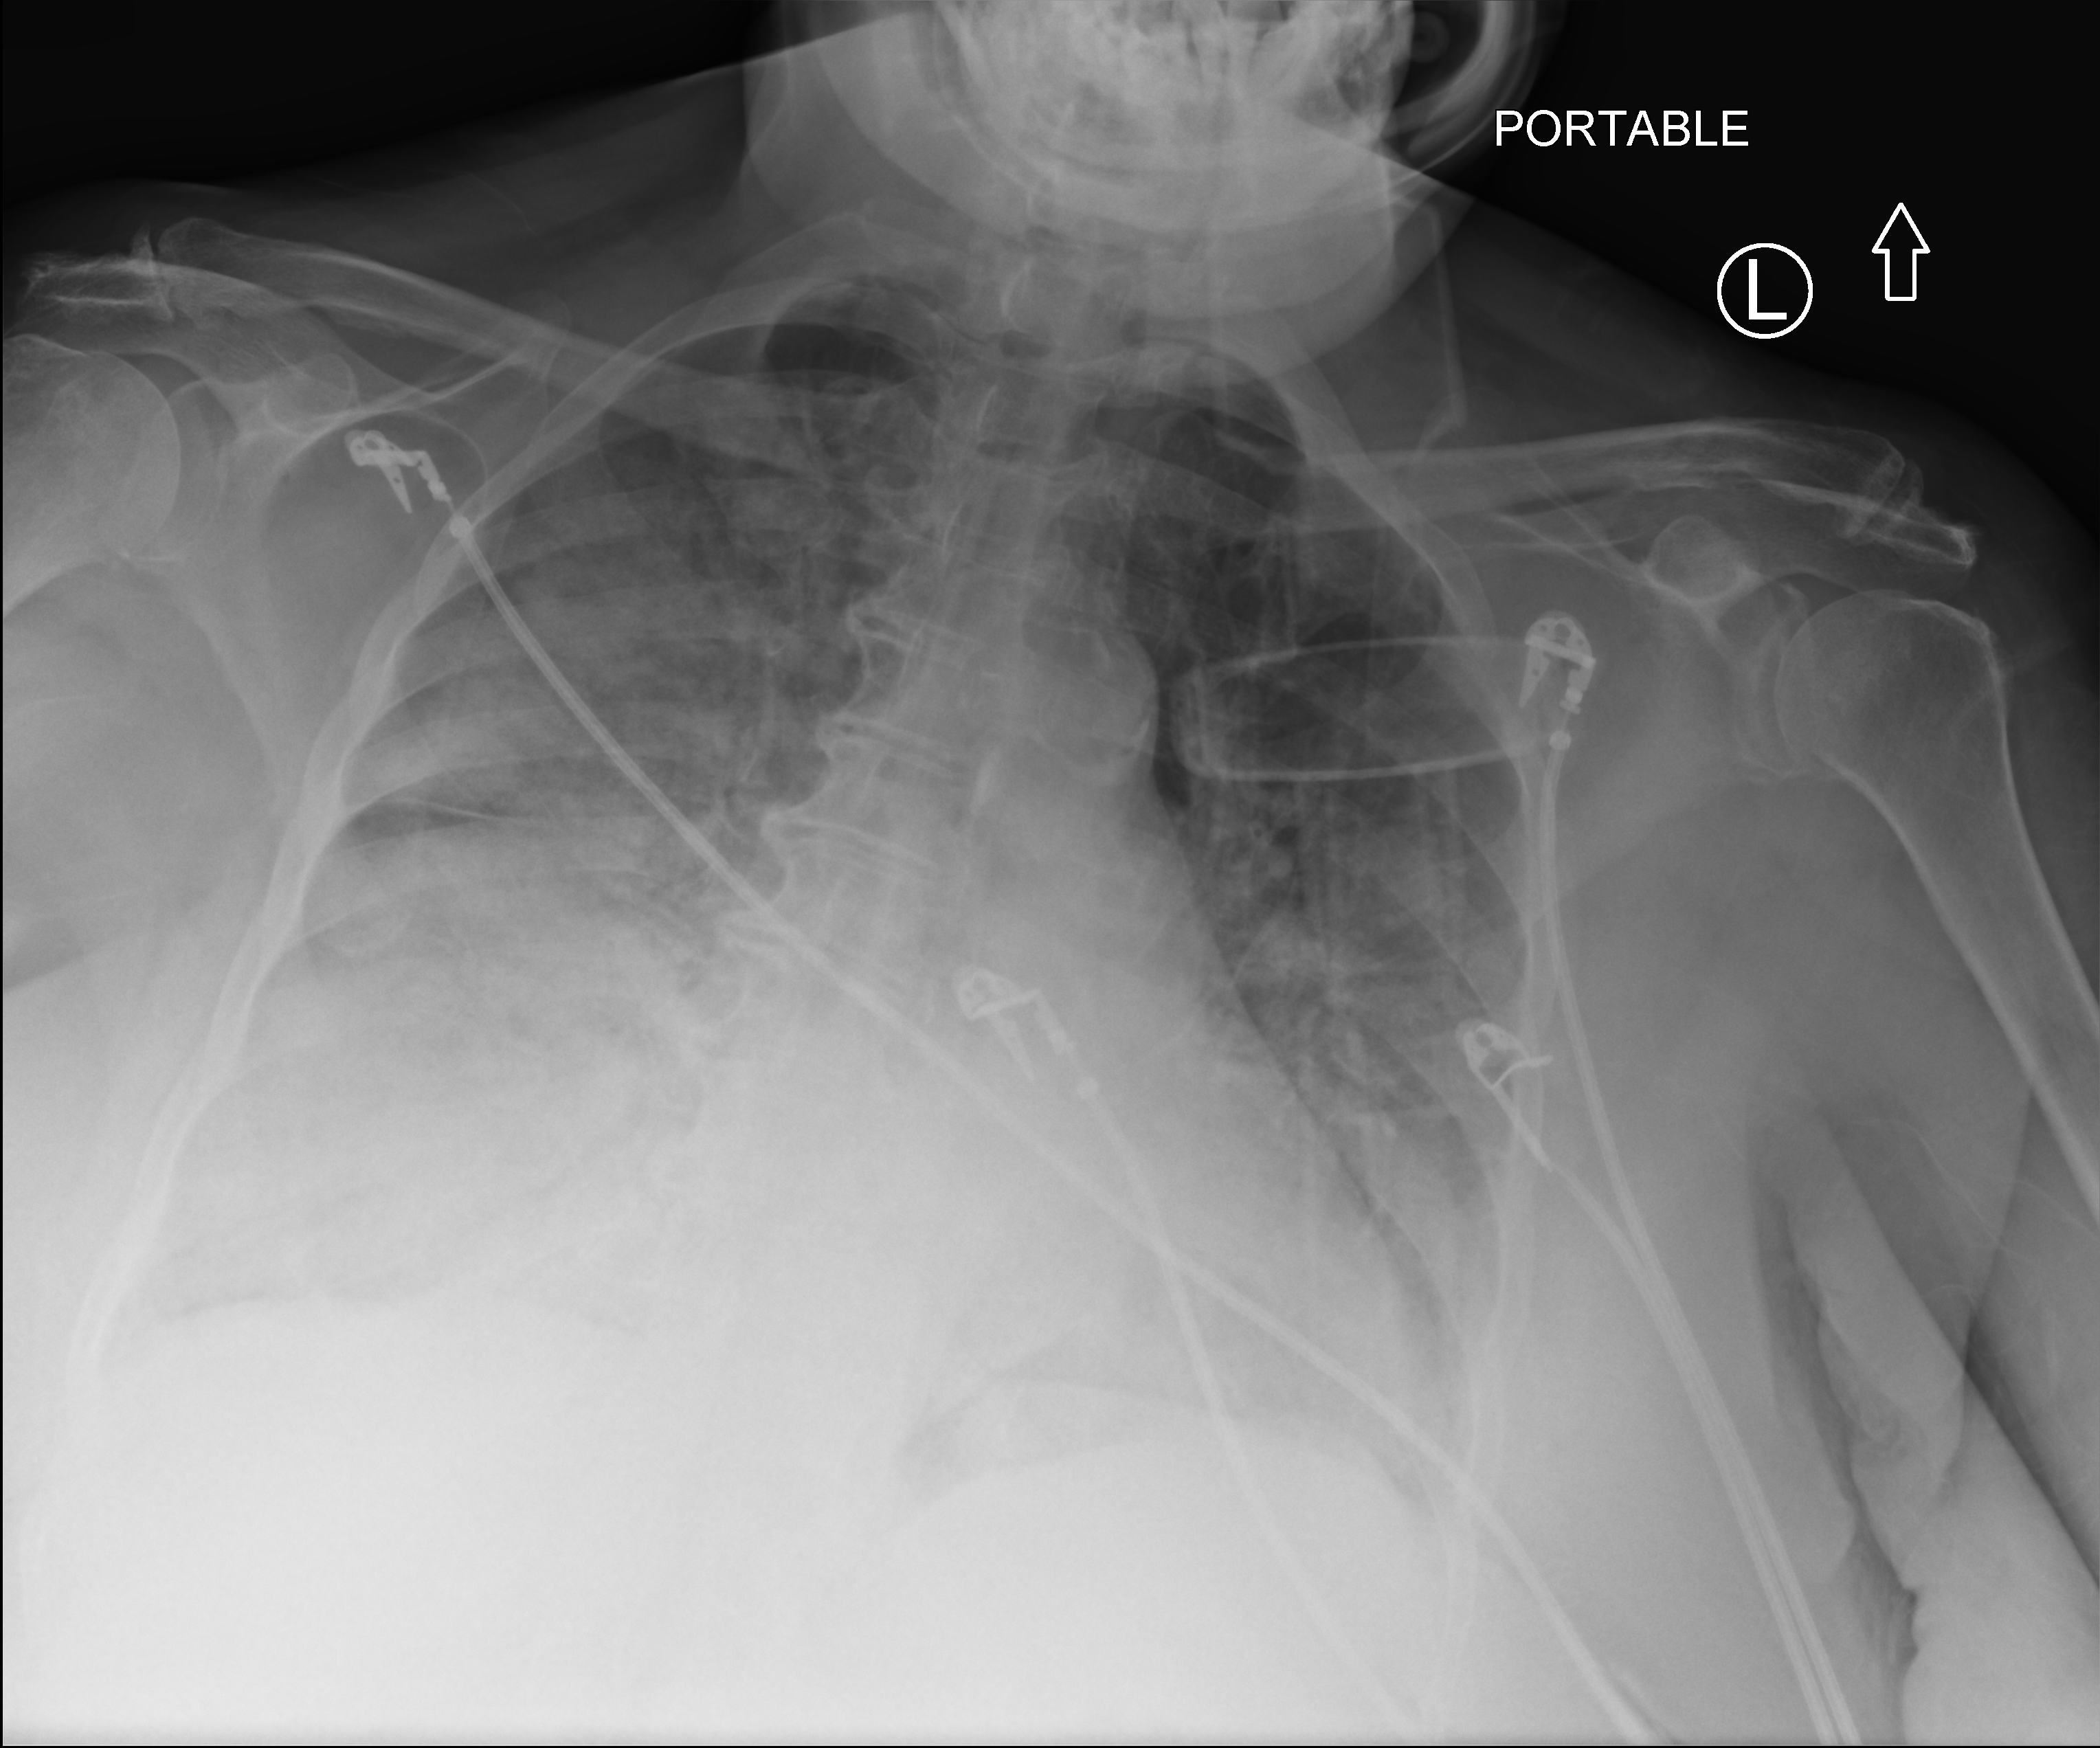
Bedside chest radiograph (computed radiography); anteroposterior (AP) projection. Patient hospitalised with COVID-19; female, aged 75–90 years.
Hospital-stay facts (about this admission, not read from this image; timing relative to this image not recorded): mechanically ventilated during this hospital stay: no; admitted to intensive care during this hospital stay: no.